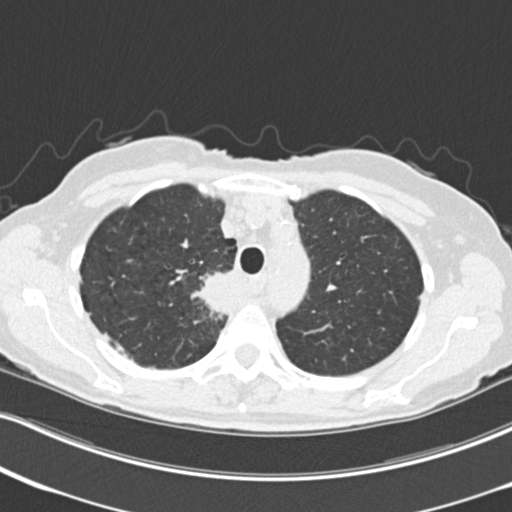
Axial slice from a low-dose chest CT screening exam. Third annual screen. Lung window (W 1500 / L -600 HU). 2 mm slice thickness. Standard (soft-tissue) reconstruction kernel (B30f). Slice 53 of 226 in the series. Female participant, aged 68 years at enrolment. Current smoker at enrolment.
• Expert-annotated lung lesion, bounding box <197,266,249,321> (left, top, right, bottom; pixels).
• Reader record for this screening exam (exam-level; its link to the box is not recorded): non-calcified nodule or mass ≥4 mm, right upper lobe, 31 × 29 mm, poorly defined margins, soft tissue attenuation, pre-existing on the prior screen: no.